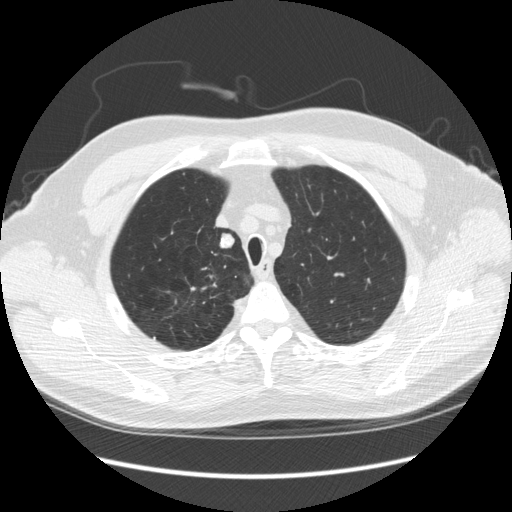
Low-dose screening chest CT, axial slice. Third screening round (two years after baseline). Lung window (W 1500 / L -600 HU). 2.5 mm slice thickness. Male, age 64 years at enrolment. Former smoker at enrolment.
Expert-annotated lung lesion, bounding box [x1, y1, x2, y2] px = [199, 230, 241, 261]. The screening reader recorded 4 non-calcified nodules or masses ≥4 mm on this exam (right upper lobe, right upper lobe, right upper lobe, right upper lobe); which of them this box marks is not recorded. Lung cancer was diagnosed 15 days after this screen: adenocarcinoma, NOS, right upper lobe, moderately differentiated (G2), stage IA (AJCC 6th edition), 14 mm at pathology.